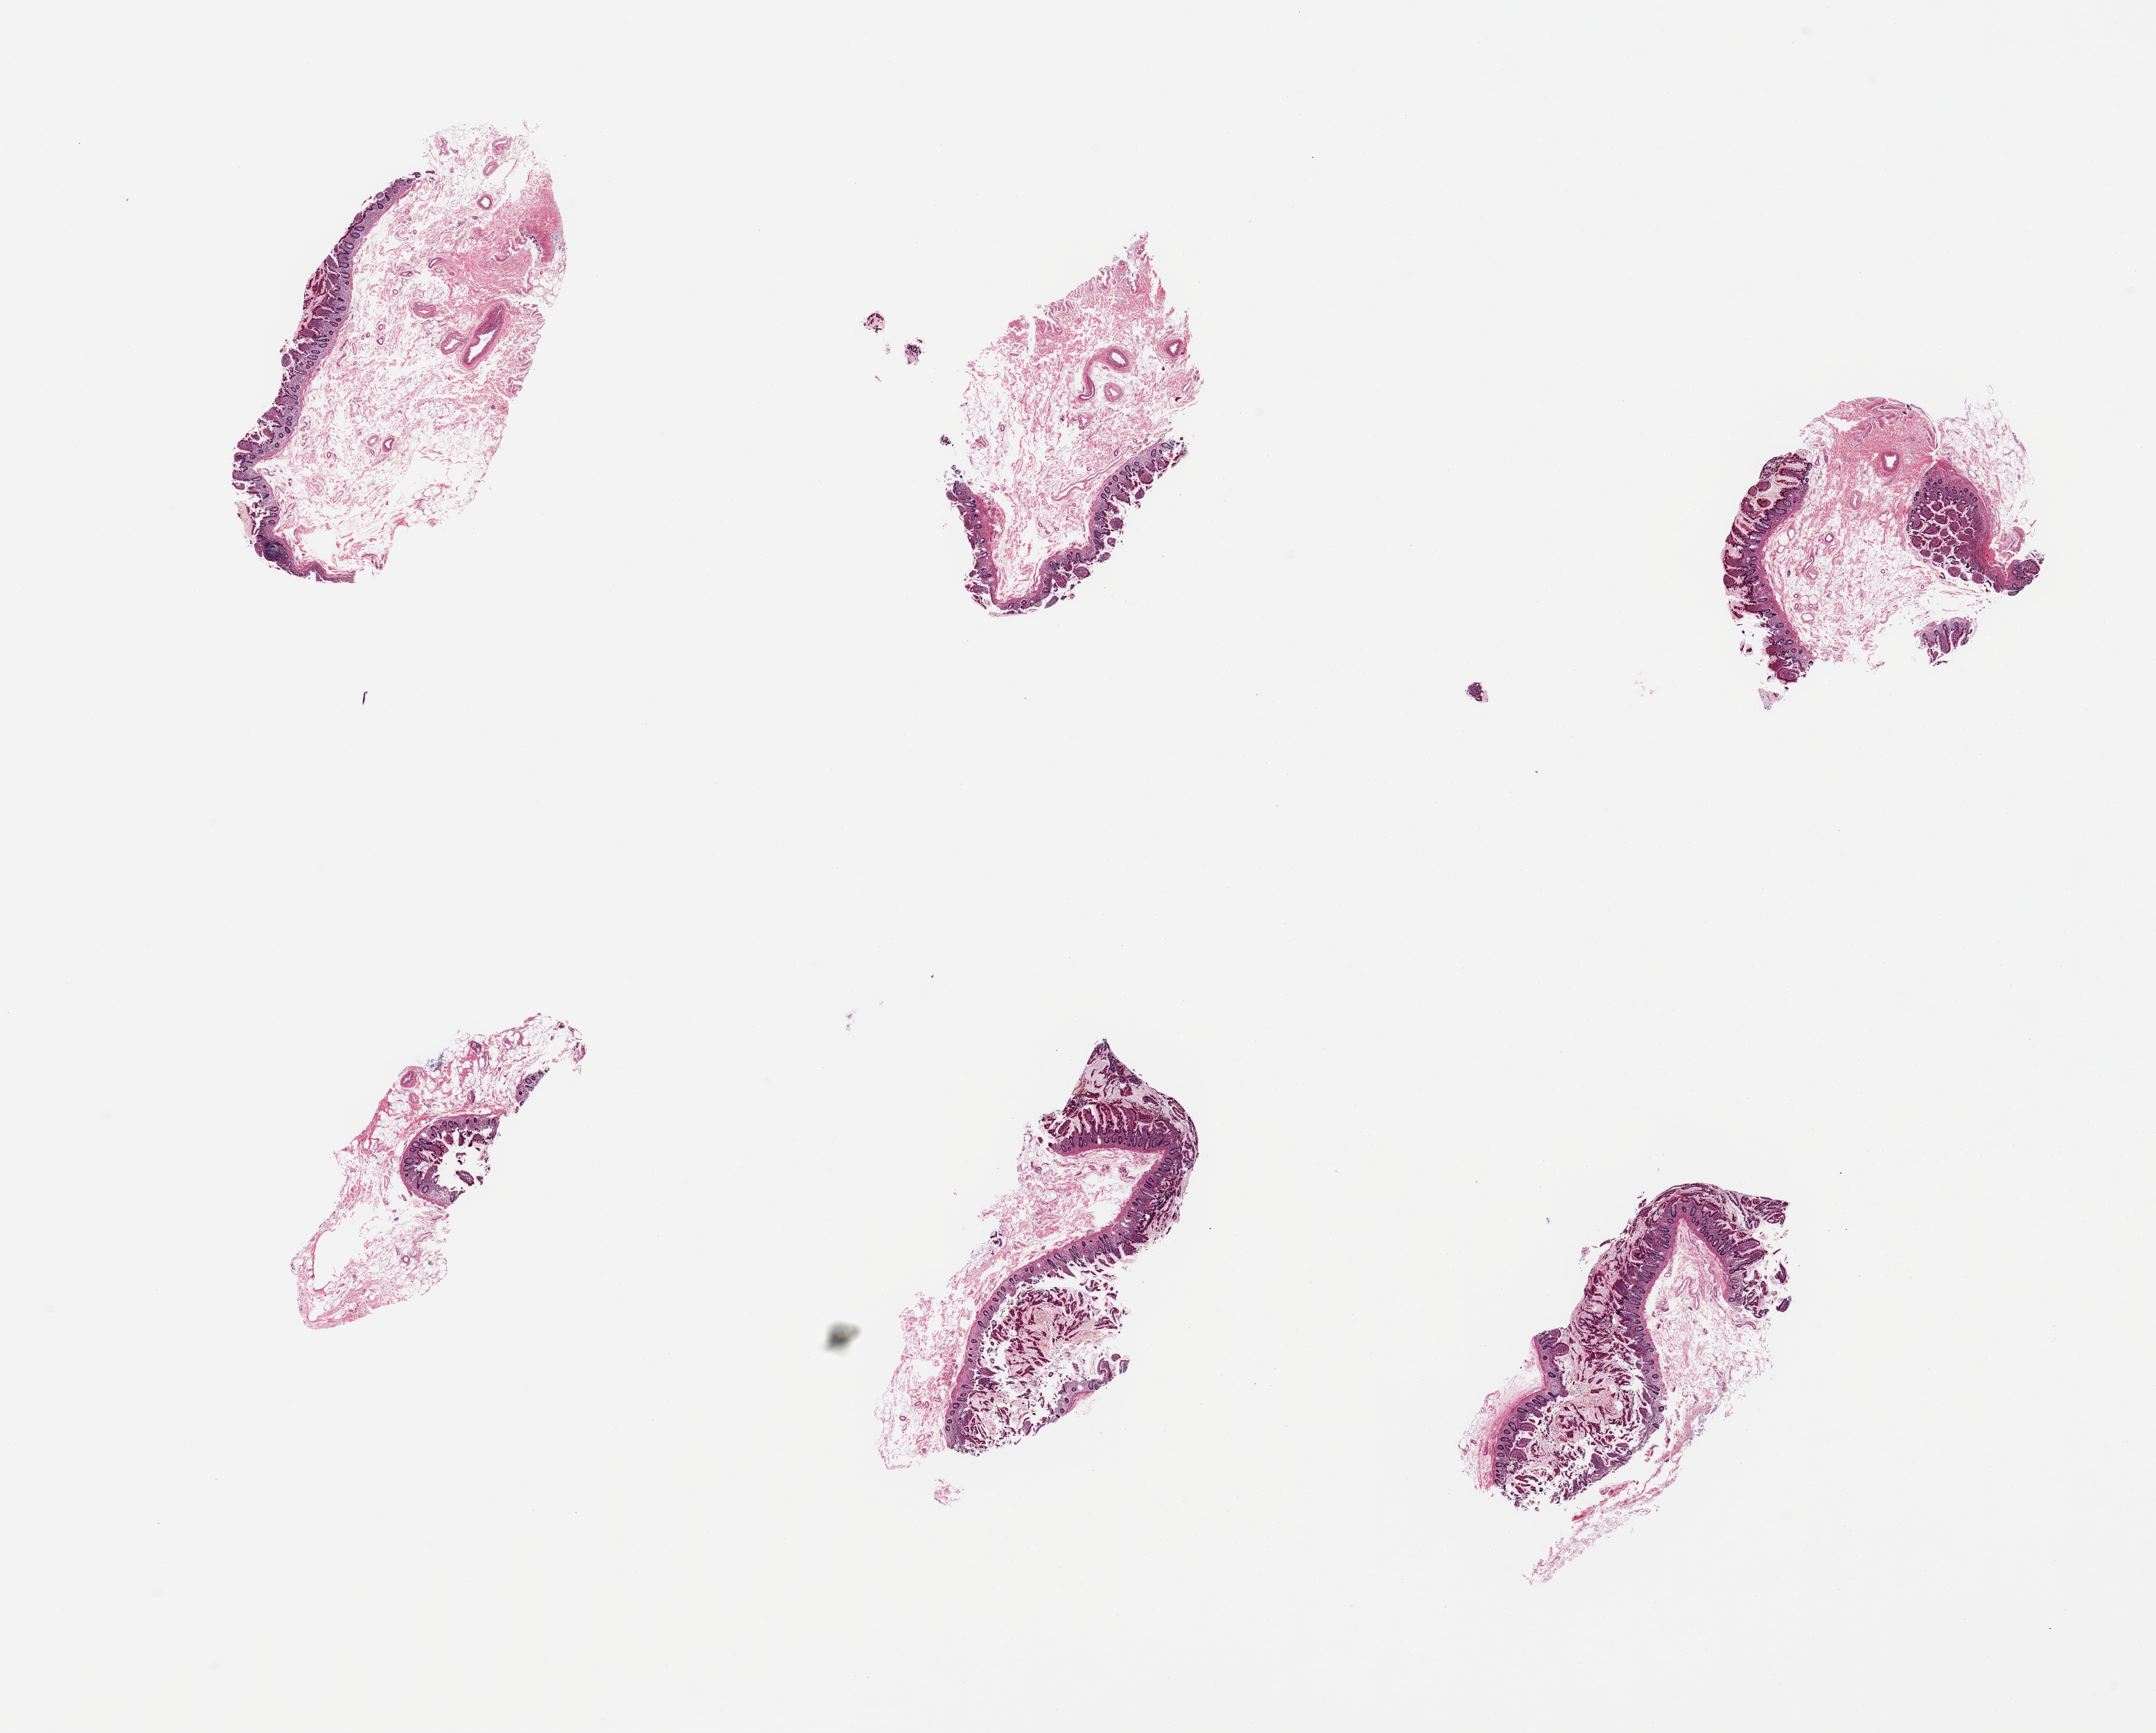
Haematoxylin and eosin whole-slide image, brightfield — a low-resolution overview of the entire scanned area, about 24.6 x 19.8 mm, PAXgene-fixed, paraffin-embedded tissue, section of ileum (target tissue), donor tissue sample. Male donor.
Pathologist's review note for this sample: 6 pieces, well - preserved mucosa, only trace lymphoid aggregates.